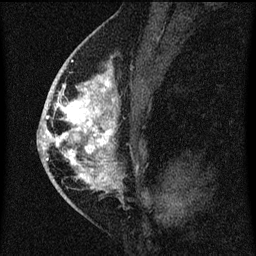
Breast MRI (dynamic contrast-enhanced), one sagittal slice. Position 37 of 60 along the scan axis. Dynamic contrast-enhanced series, image 2 of 3 at this slice position (ordered by acquisition). 1.5 T. TE 4.2 ms, TR 8 ms. 2 mm slice thickness. 256 × 256 image matrix, field of view 180 × 180 mm. Female patient, age 46 years.
Structures marked on this image (semi-automatically segmented with operator editing):
- analysis volume of interest (the breast-tissue region the enhancement analysis was run in; not a lesion): bounding box <48,68,118,195> (left, top, right, bottom; pixels)
- tumour enhancement mask (voxels above the 70 % enhancement threshold inside the analysis volume of interest): <48,68,118,191>